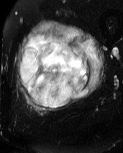
MRI of an extremity soft-tissue mass, one axial slice. Slice 20 of 60 in the series (ordered by position). T2-weighted fat-saturated. MR volume resampled by the dataset authors to the PET/CT grid (not the native acquisition matrix). 3.27 mm slice thickness. 123 × 153 image matrix. Male patient. Case-level facts recorded for this patient, not image findings: histological type: pleiomorphic liposarcoma; grade: high; site of the primary tumour: left thigh.
Outlined on this slice (expert contour drawn on MRI and transferred to this co-registered scan by the dataset authors):
- gross tumour volume including surrounding oedema: bounding box (x1, y1, x2, y2) in pixels: (15, 22, 105, 114)
- gross tumour volume (mass): (20, 33, 91, 108)